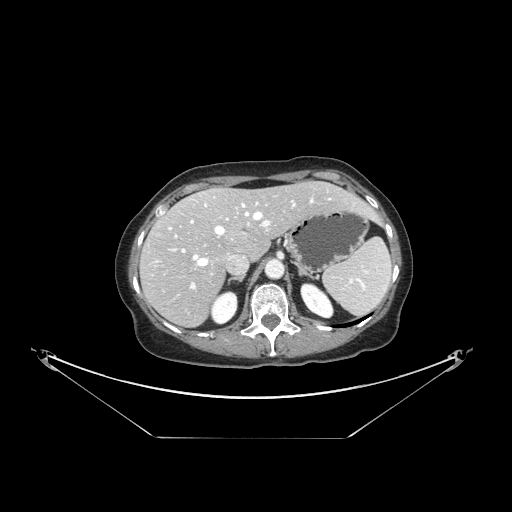
Contrast-enhanced abdominal CT, one axial slice; slice 102 of 148 in the series (ordered by position); reconstruction kernel STANDARD; intravenous contrast given; soft-tissue window (W 400 / L 40 HU); 2.5 mm slice thickness; 512 × 512 image matrix, field of view 500 × 500 mm. Female patient, age 73 years. From the clinical record (not read from this slice): diagnosis: colorectal cancer liver metastases, imaged before liver resection; multiple liver metastases: no; largest metastasis: 1 cm; disease in both lobes: no.
Outlined on this slice (manually delineated by an expert):
- hepatic veins: bounding box <169,198,331,266> (left, top, right, bottom; pixels)
- liver: <142,182,374,326>
- planned liver remnant (the part of the liver to remain after resection): <168,182,373,258>
- portal vein (with intrahepatic branches): <171,204,270,289>